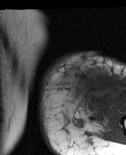
MRI of an extremity soft-tissue mass, one axial slice. Slice 19 of 86 in the series (ordered by position). MR volume resampled by the dataset authors to the PET/CT grid (not the native acquisition matrix). 126 × 155 image matrix, field of view 123 × 151 mm. Female patient. From the clinical record (not read from this slice): histological type: pleiomorphic leiomyosarcoma; grade: high; site of the primary tumour: left biceps.
Outlined on this slice (expert contour drawn on MRI and transferred to this co-registered scan by the dataset authors):
- gross tumour volume including surrounding oedema: bounding box (x1, y1, x2, y2) in pixels: (63, 70, 119, 112)
- gross tumour volume (mass): (63, 70, 114, 94)